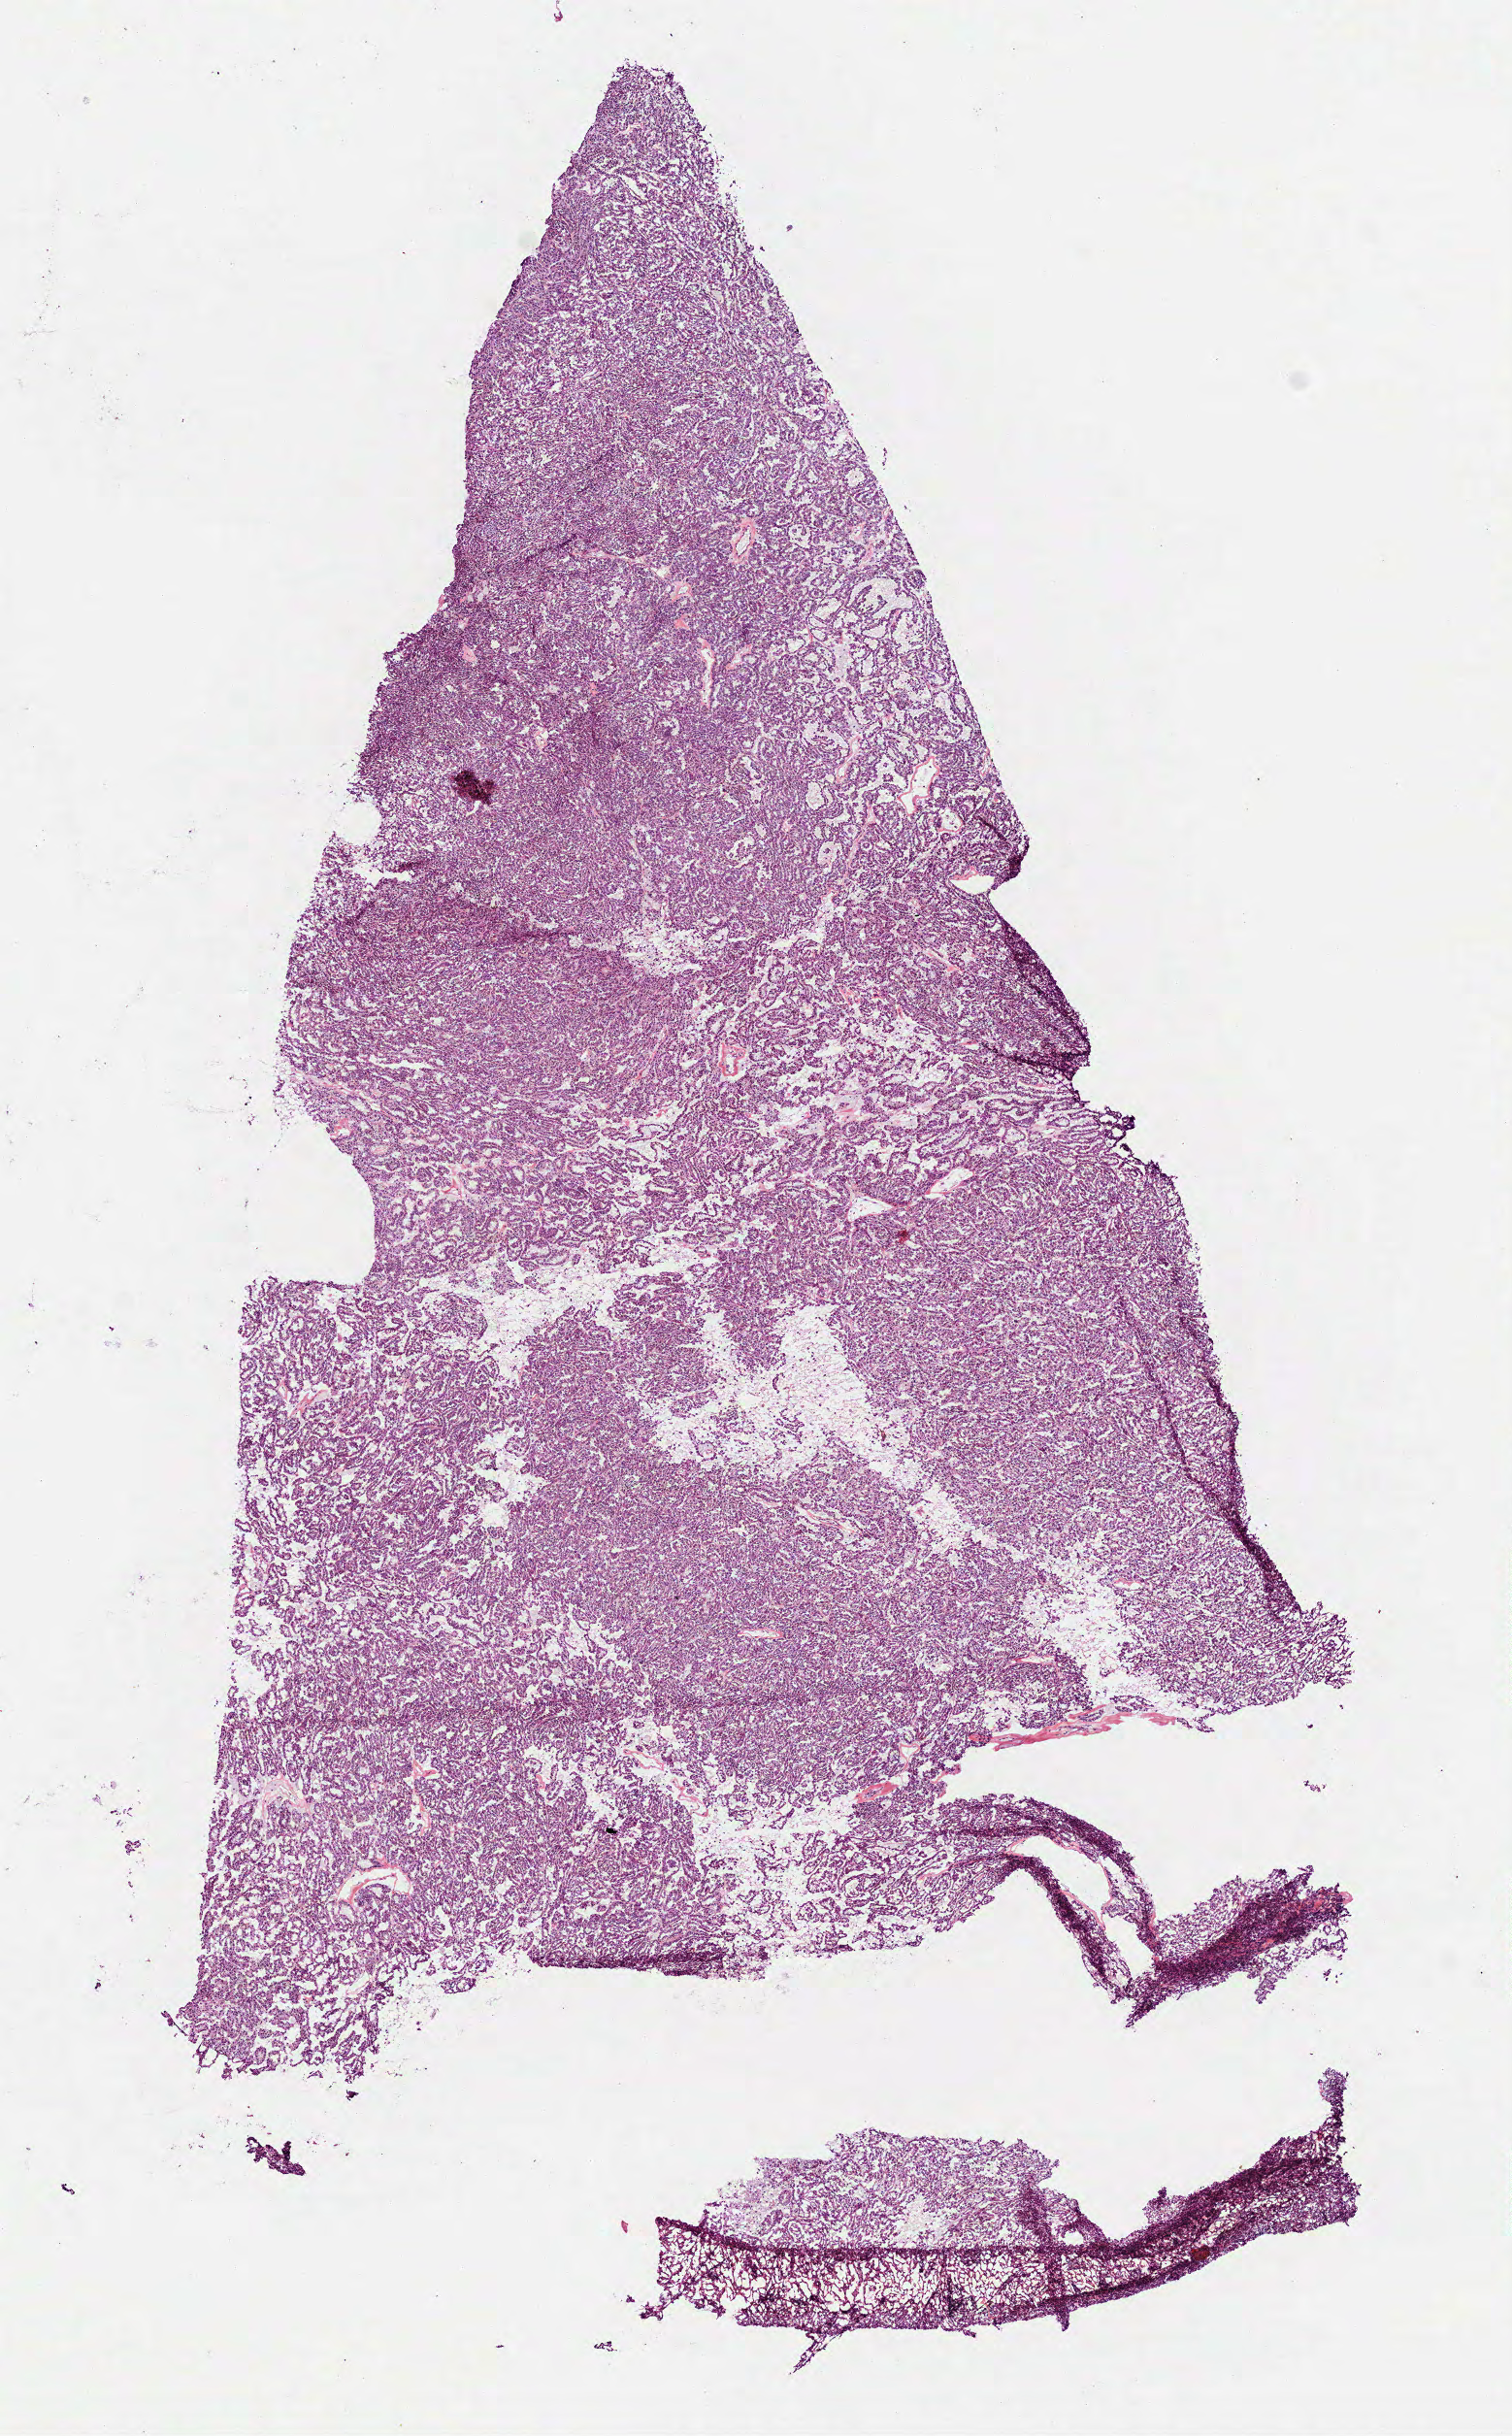
H&E-stained whole-slide image, a low-resolution overview of the entire scanned area, about 6.3 x 10.1 mm (acquisition: 40x scan). Frozen section from the top of the tissue portion. Kidney, primary tumour sample. Patient: male, age at initial diagnosis 59 years. Composition of this section per pathologist review: tumour cells 100%, tumour nuclei 90%, normal cells 0%, stromal cells 0%, necrosis 0%. Infiltration values recorded for this section: lymphocyte infiltration 0%, monocyte infiltration 1%, neutrophil infiltration 0%.
AJCC pathologic stage: II (7th edition). Laterality: left. Diagnosis: Papillary adenocarcinoma, NOS.